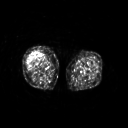
FDG PET of an extremity soft-tissue mass (from a PET/CT study), one axial slice; slice 217 of 311 in the series (ordered by position); 3.27 mm slice thickness; 128 × 128 image matrix, field of view 500 × 500 mm. Female patient, age 57 years. From the clinical record (not read from this slice): histological type: pleiomorphic undifferentiated sarcoma; grade: high; site of the primary tumour: right quadricep.
Outlined on this slice (expert contour drawn on MRI and transferred to this co-registered scan by the dataset authors):
- tumour plus oedema (research contour): bounding box <26,52,41,68> (left, top, right, bottom; pixels)